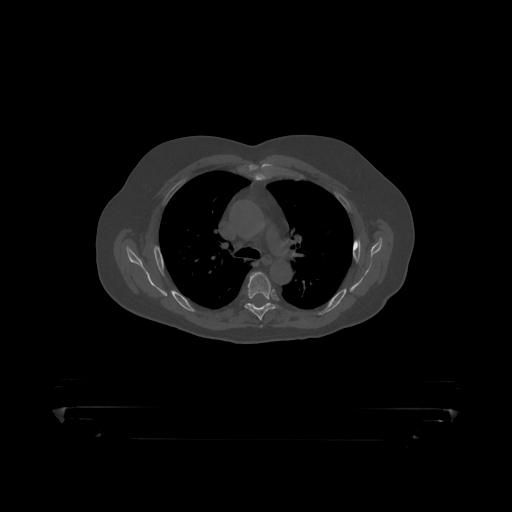
CT including the spine, one axial slice. 120 kVp. Bone window (W 1800 / L 400 HU). 512 × 512 image matrix. Male patient, age 60 years. From the clinical record (not read from this slice): primary cancer: prostate.
Outlined on this slice (semi-automatic segmentation, software-assisted and operator-edited):
- T5 vertebra: box from (x=245, y=272) to (x=275, y=319) px
- T6 vertebra: (x=250, y=304)–(x=274, y=308)